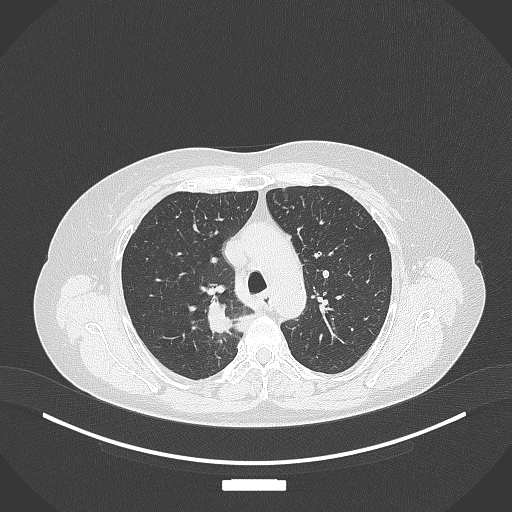
Chest CT, one axial slice. Position 276 of 357 along the scan axis. Reconstruction kernel B70f. Lung window (W 1500 / L -600 HU). 1 mm slice thickness. 512 × 512 image matrix, field of view 400 × 400 mm. Patient: female, 62 years. From the clinical record (not read from this slice): clinical TNM (as recorded): T1c N1 M0.
Annotated regions visible in this slice (rectangle marked by the reading radiologist):
- lung tumour (recorded histology: squamous cell carcinoma): bounding box [x1, y1, x2, y2] px = [203, 298, 236, 336]